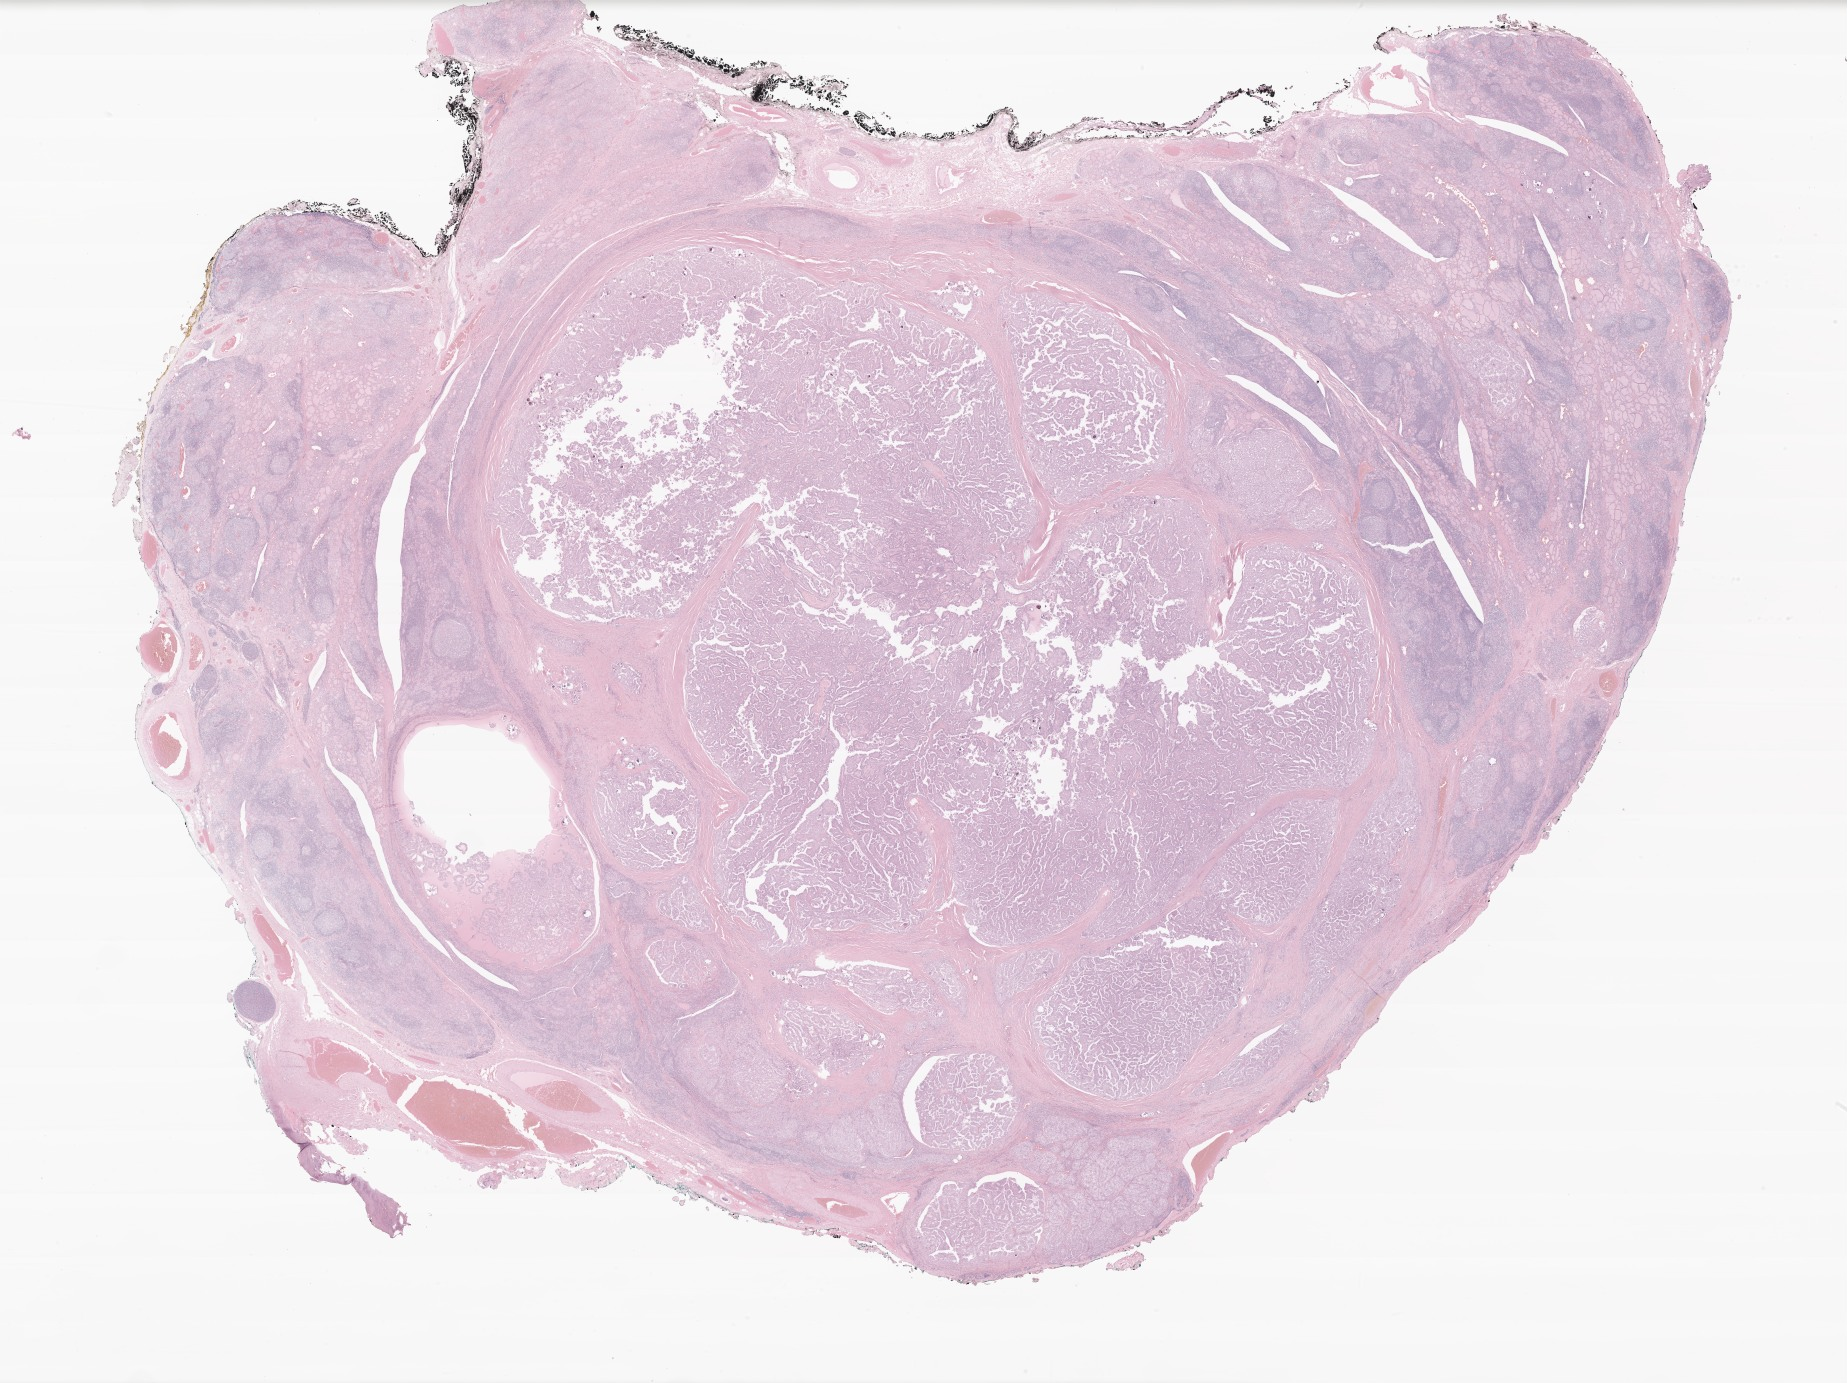
Whole-slide image, haematoxylin and eosin stain of tumor tissue from the thyroid — a low-resolution overview of the entire scanned area, about 31.1 x 23.3 mm, formalin-fixed, paraffin-embedded (FFPE) tissue. Female patient, age 167 months (13 years 11 months).
Diagnosis: Papillary carcinoma, NOS.